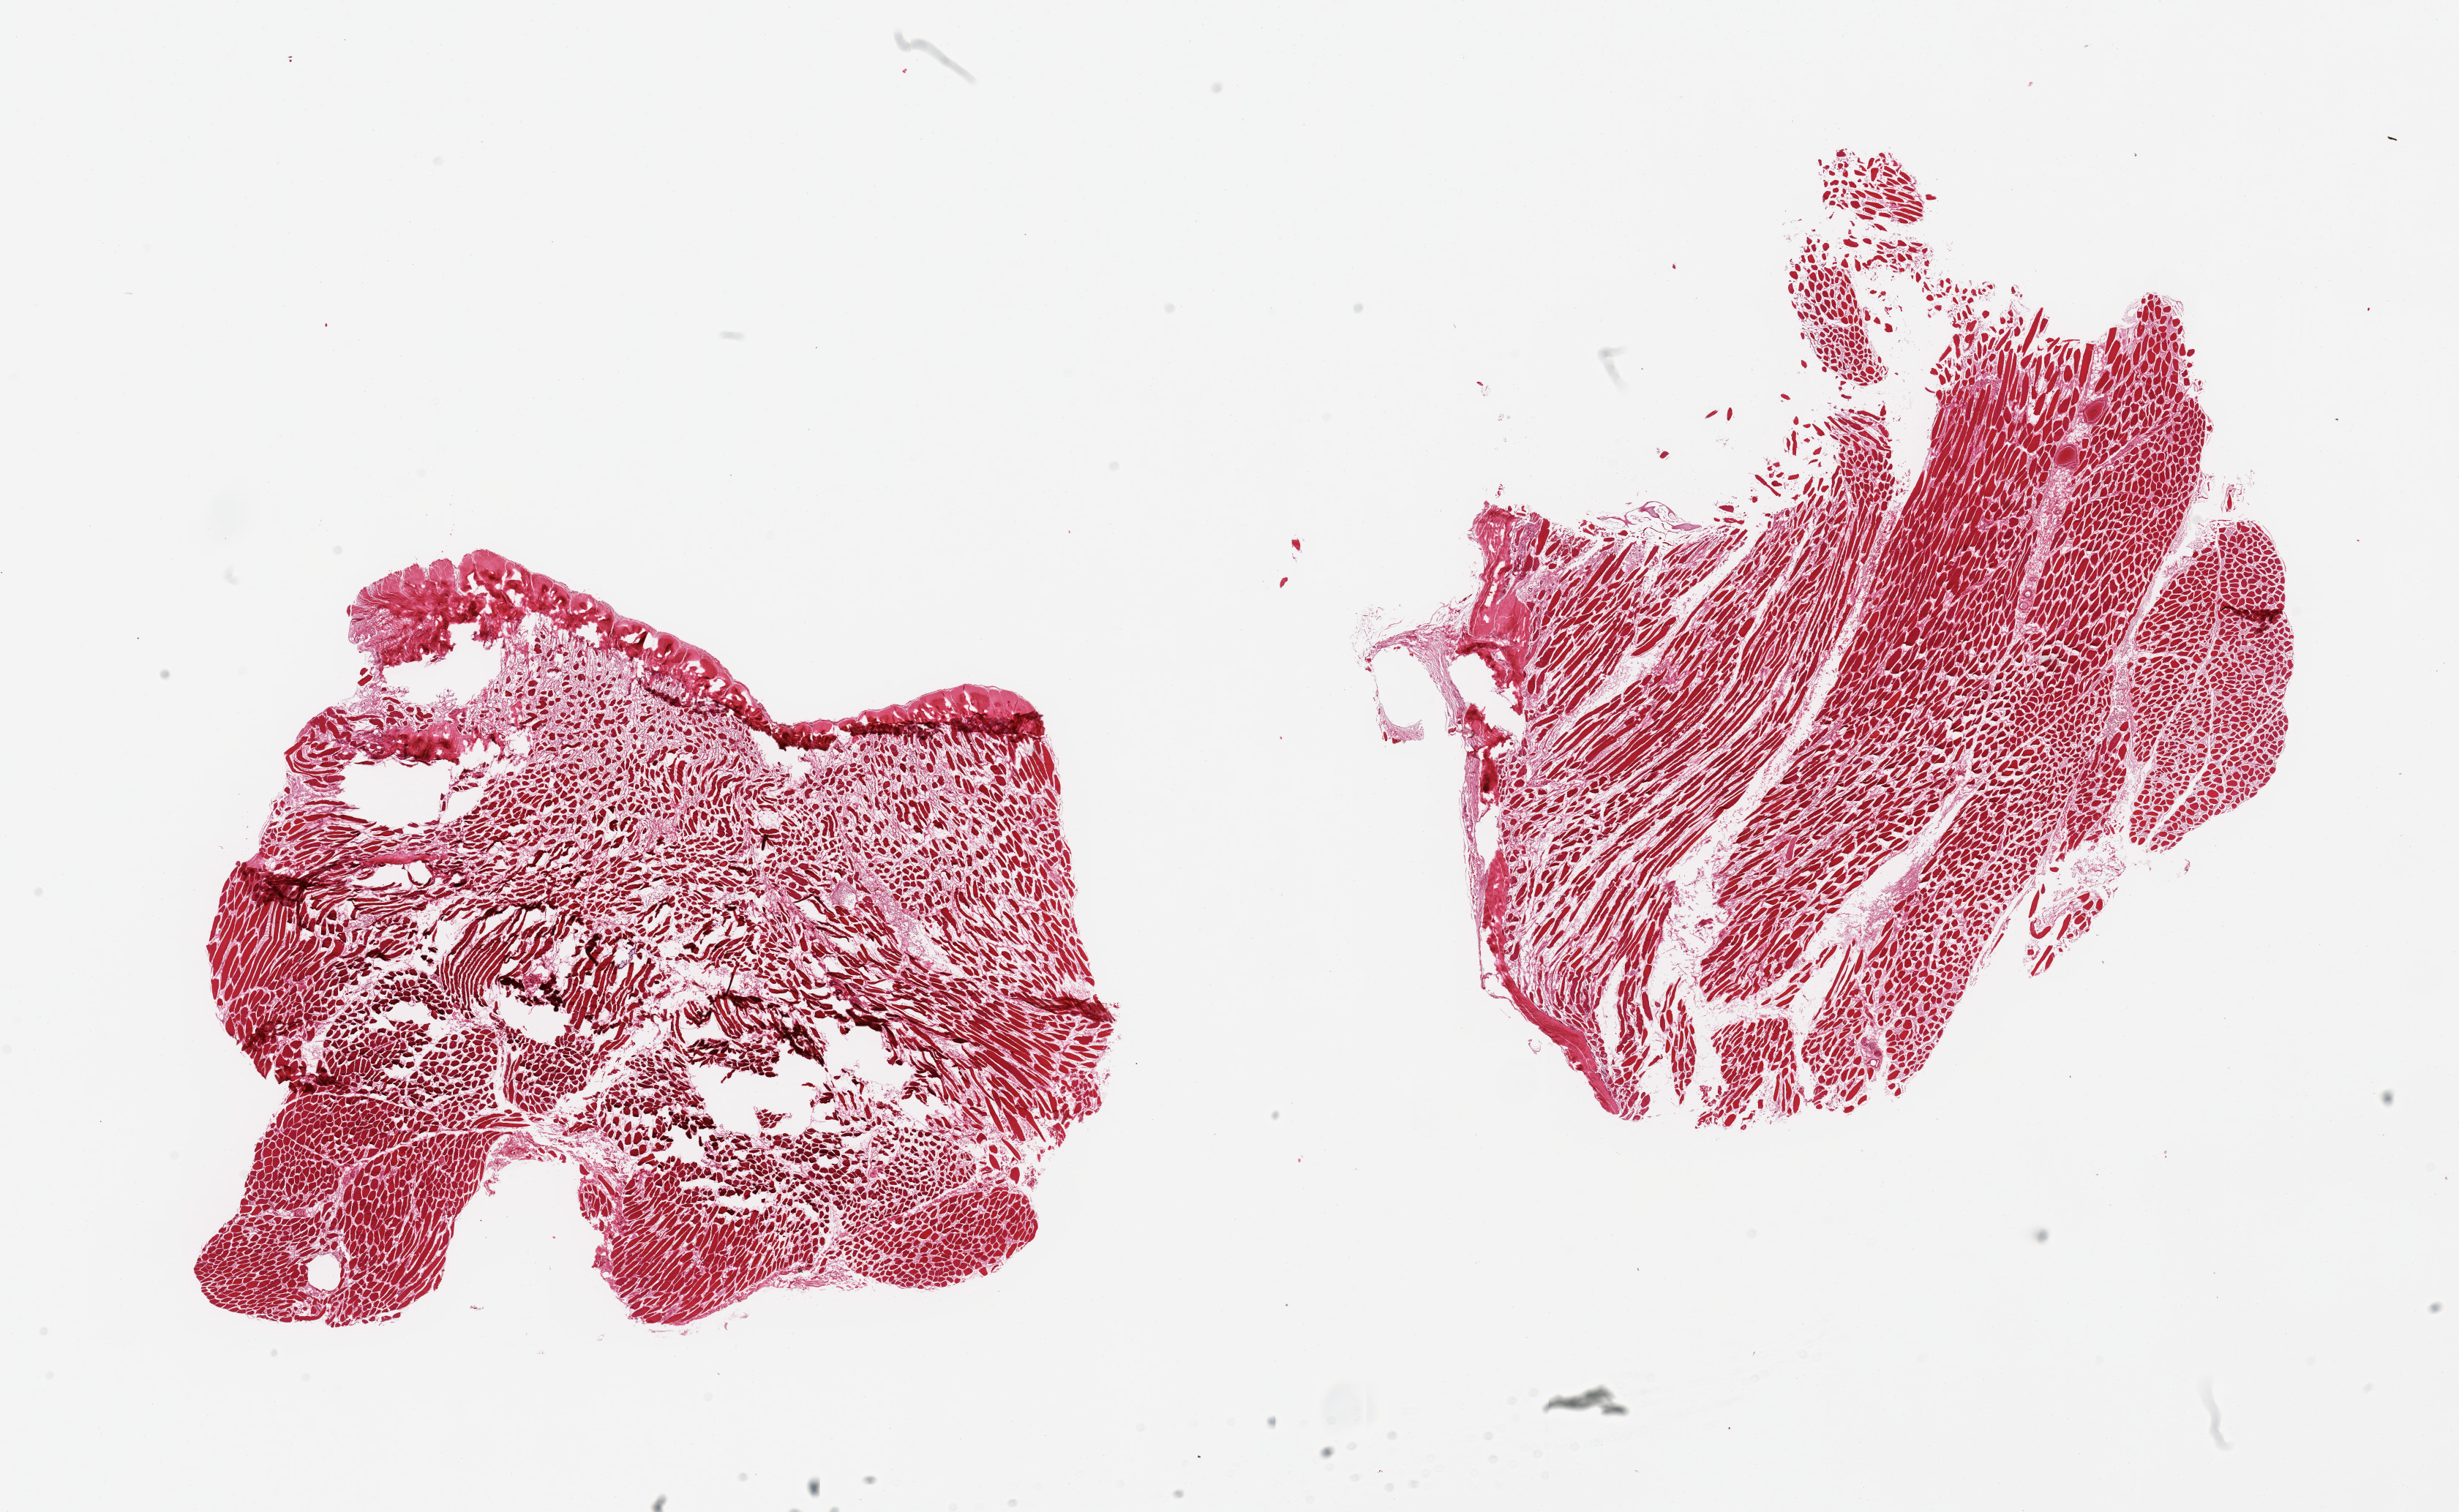
Hematoxylin and eosin (H&E) whole-slide image, whole scanned area (about 26.6 x 16.3 mm, acquisition: 20x scan) shown as a low-resolution overview; PAXgene-fixed, paraffin-embedded tissue; sampled site (target tissue): skeletal muscle; donor tissue sample. Female donor.
Review note (as recorded): 2 pieces, ? poor fixation.